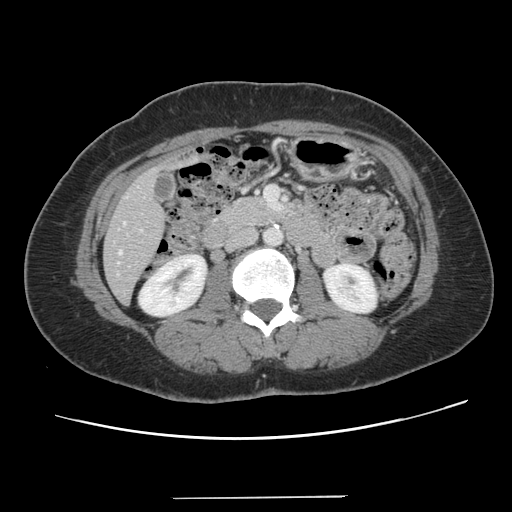
Contrast-enhanced abdominal CT, one axial slice. Position 42 of 141 along the scan axis. Soft-tissue window (W 400 / L 40 HU). 2.5 mm slice thickness. 512 × 512 image matrix, field of view 366 × 366 mm. Female patient, age 53 years. From the clinical record (not read from this slice): diagnosis: colorectal cancer liver metastases, imaged before liver resection; multiple liver metastases: no; largest metastasis: 14.5 cm.
Outlined on this slice (expert manual segmentation):
- hepatic veins: bounding box [x1, y1, x2, y2] px = [119, 251, 121, 254]
- liver: [104, 165, 167, 302]
- planned liver remnant (the part of the liver to remain after resection): [104, 216, 165, 303]